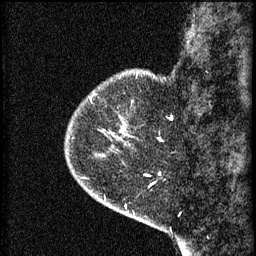
Breast MRI (dynamic contrast-enhanced), one sagittal slice; 3 images stored at this slice position (order not interpretable as contrast timing); 1.5 T; TE 4.2 ms, TR 8.2 ms; 2 mm slice thickness; 256 × 256 image matrix. Patient: female, 44 years.
Outlined on this slice (semi-automatically segmented with operator editing):
- analysis volume of interest (the breast-tissue region the enhancement analysis was run in; not a lesion): bounding box [x1, y1, x2, y2] px = [73, 82, 135, 155]
- tumour enhancement mask (voxels above the 70 % enhancement threshold inside the analysis volume of interest): [121, 132, 128, 135]